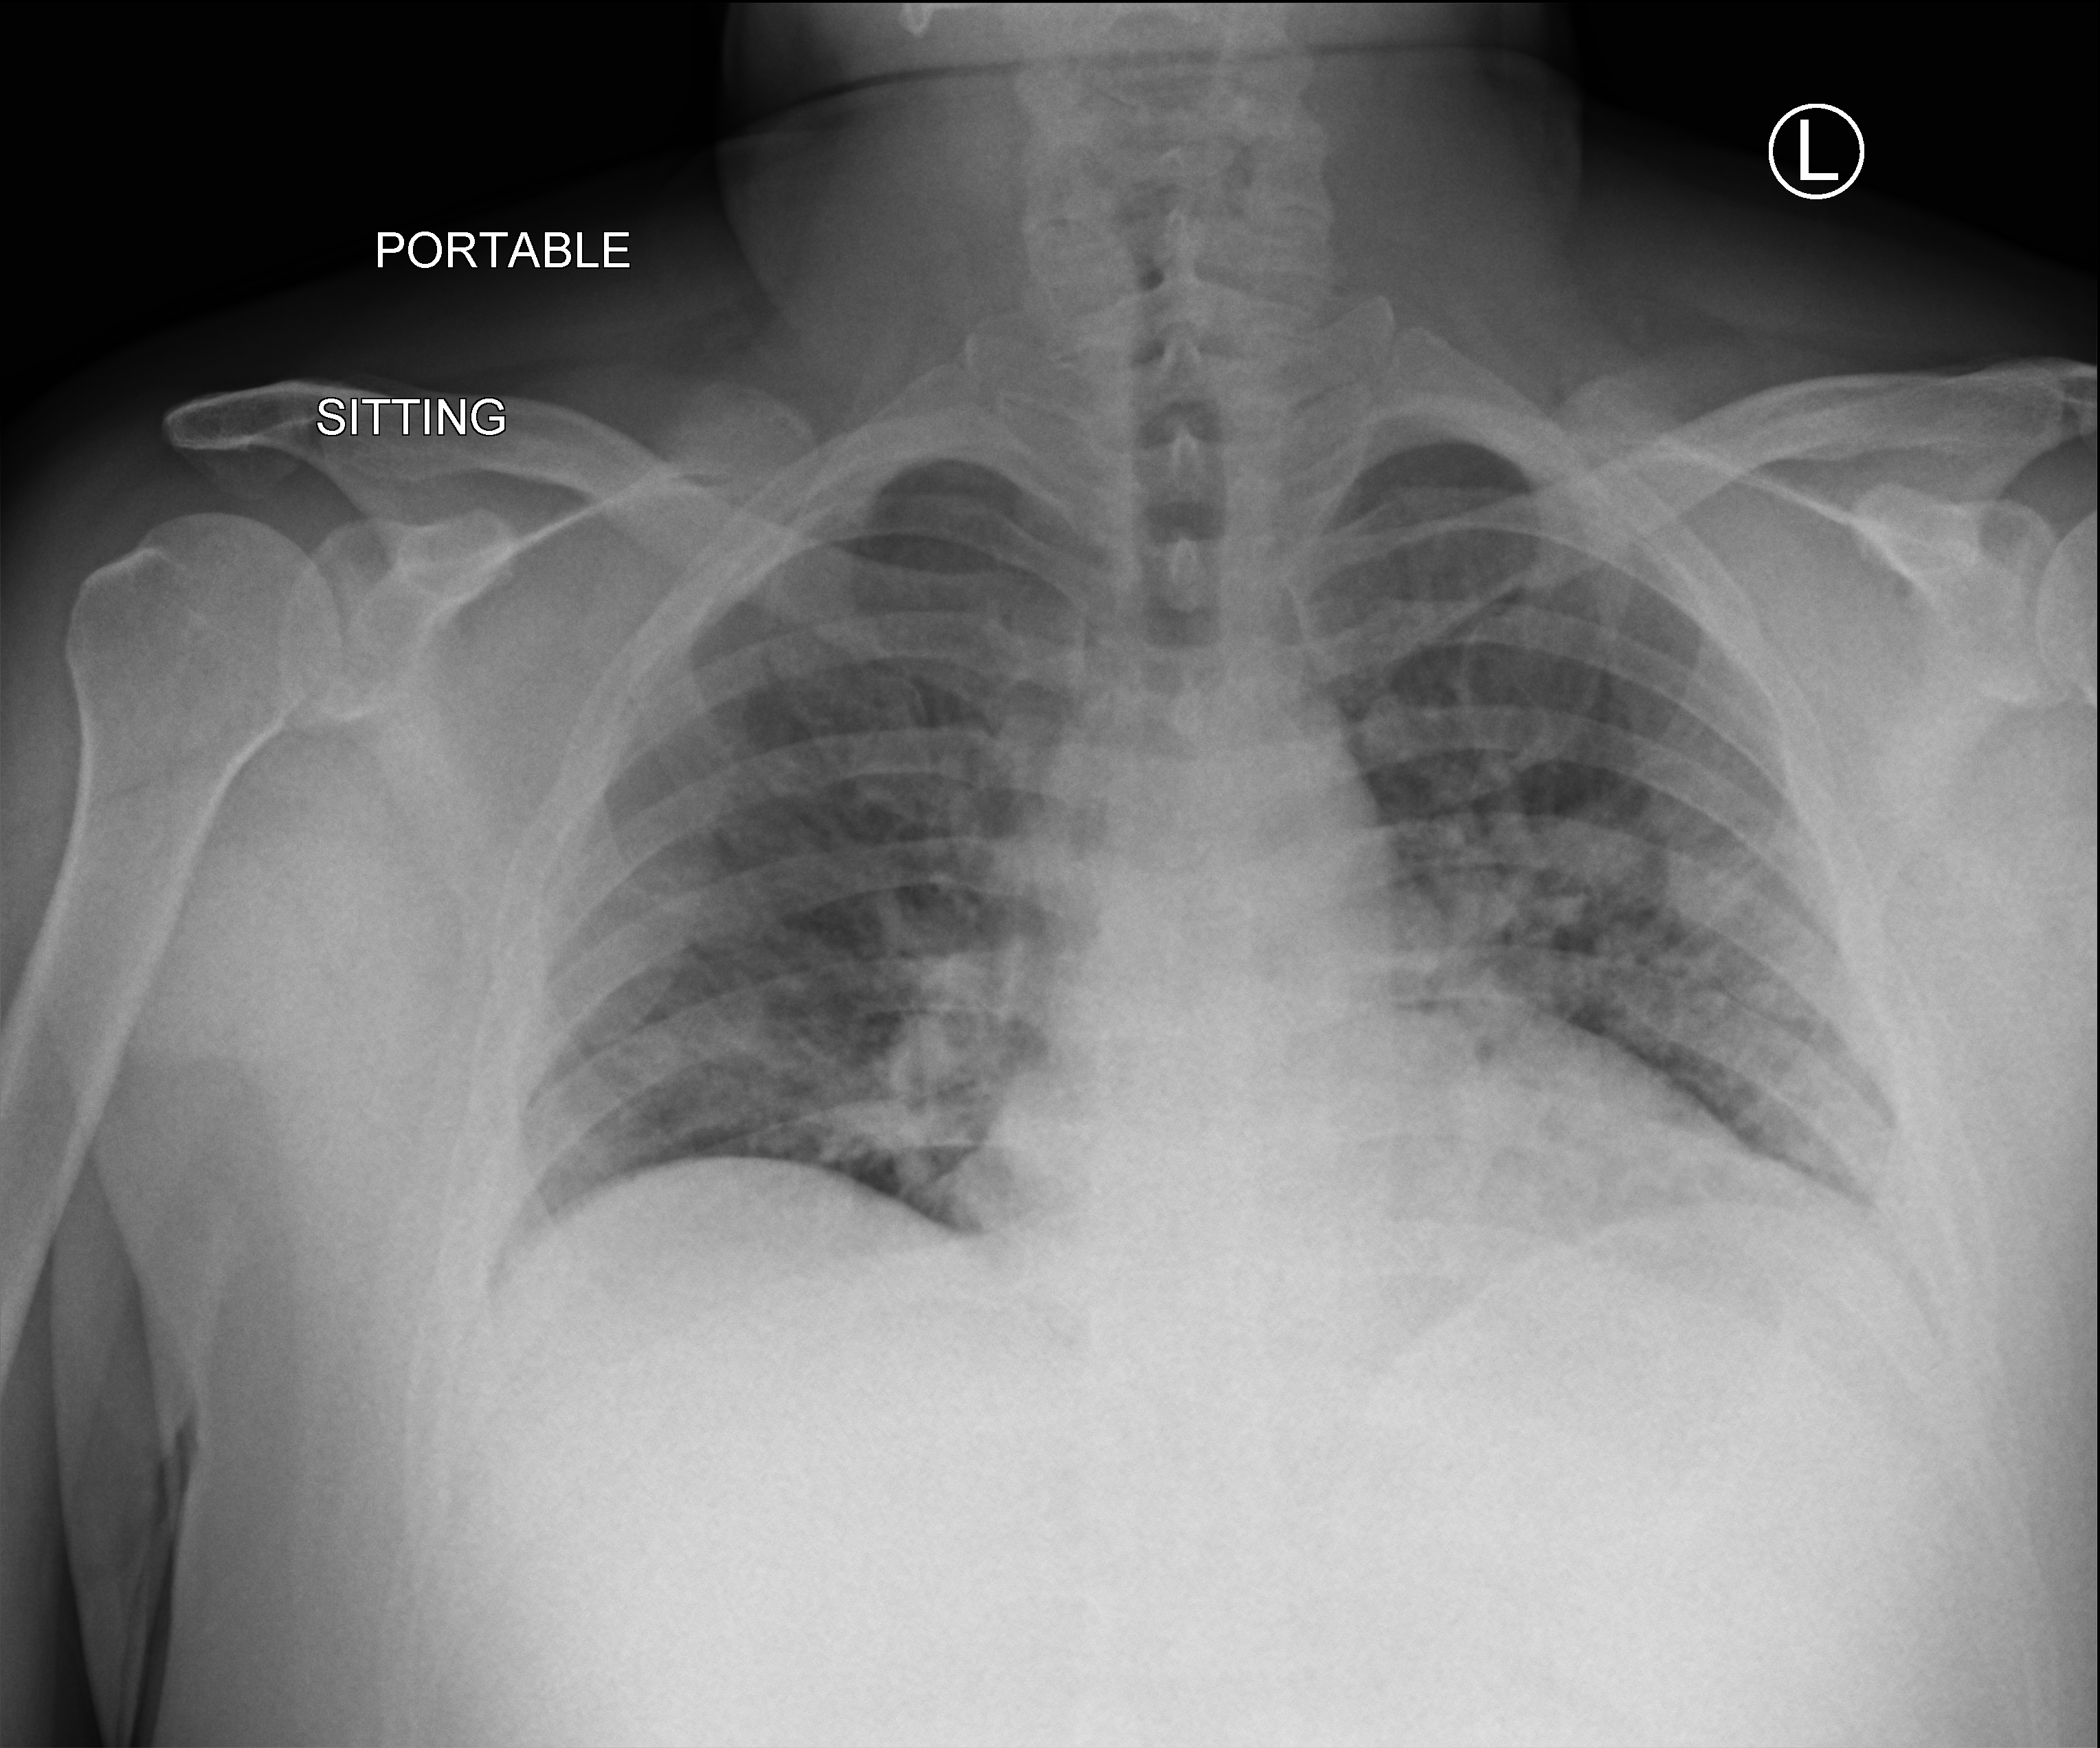
Bedside chest radiograph (computed radiography); anteroposterior (AP) projection. Patient hospitalised with COVID-19; male, aged 18–59 years.
From the hospital-stay record, not from the radiograph (when in the stay this image was taken is not recorded): COPD (admission record): no.